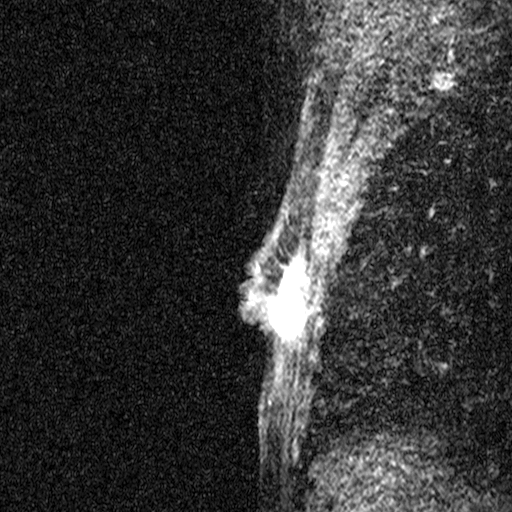
Breast MRI (dynamic contrast-enhanced), one sagittal slice. Slice 30 of 44 in the series (ordered by position). Dynamic contrast-enhanced study with each time point stored as its own series, time point 2 of 3 at this slice position (early post-contrast, ordered by acquisition time). 1.5 T. TE 4.5 ms, TR 11 ms. 512 × 512 image matrix, field of view 200 × 200 mm. Patient: female, 45 years. From the clinical record (not read from this slice): setting: breast cancer imaged before/during neoadjuvant chemotherapy; receptor status: HR-positive, HER2-negative.
Annotated regions visible in this slice (semi-automatically segmented with operator editing):
- analysis volume of interest (the breast-tissue region the enhancement analysis was run in; not a lesion): bounding box (x1, y1, x2, y2) in pixels: (256, 218, 313, 359)
- tumour enhancement mask (voxels above the 90 % enhancement threshold inside the analysis volume of interest): (257, 243, 311, 332)